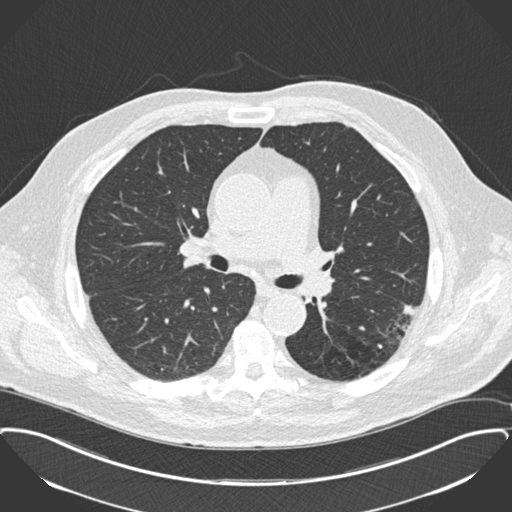
Low-dose screening chest CT, one axial slice. 120 kVp. Lung window (W 1500 / L -600 HU). 512 × 512 image matrix, field of view 400 × 400 mm.
Structures marked on this image (manually delineated by an expert):
- lesion 1 (tumor, lower lobe of left lung): box from (x=403, y=305) to (x=414, y=316) px